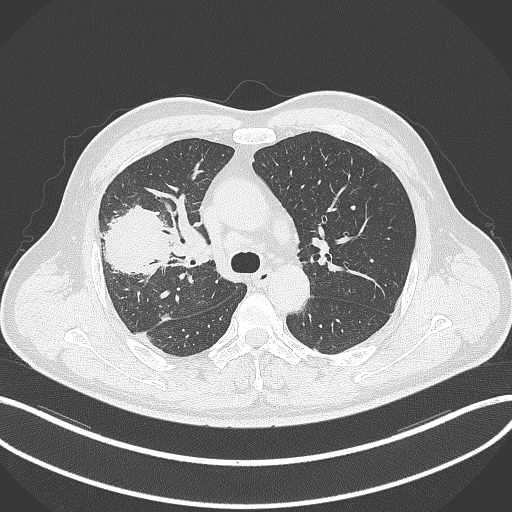
Chest CT, one axial slice; 120 kVp; lung window (W 1500 / L -600 HU); 1 mm slice thickness; 512 × 512 image matrix. Patient: male, 55 years. From the clinical record (not read from this slice): clinical TNM (as recorded): T3 N2 M1.
Annotated regions visible in this slice (bounding box drawn by a radiologist):
- lung tumour (recorded histology: adenocarcinoma): bounding box <96,204,179,279> (left, top, right, bottom; pixels)